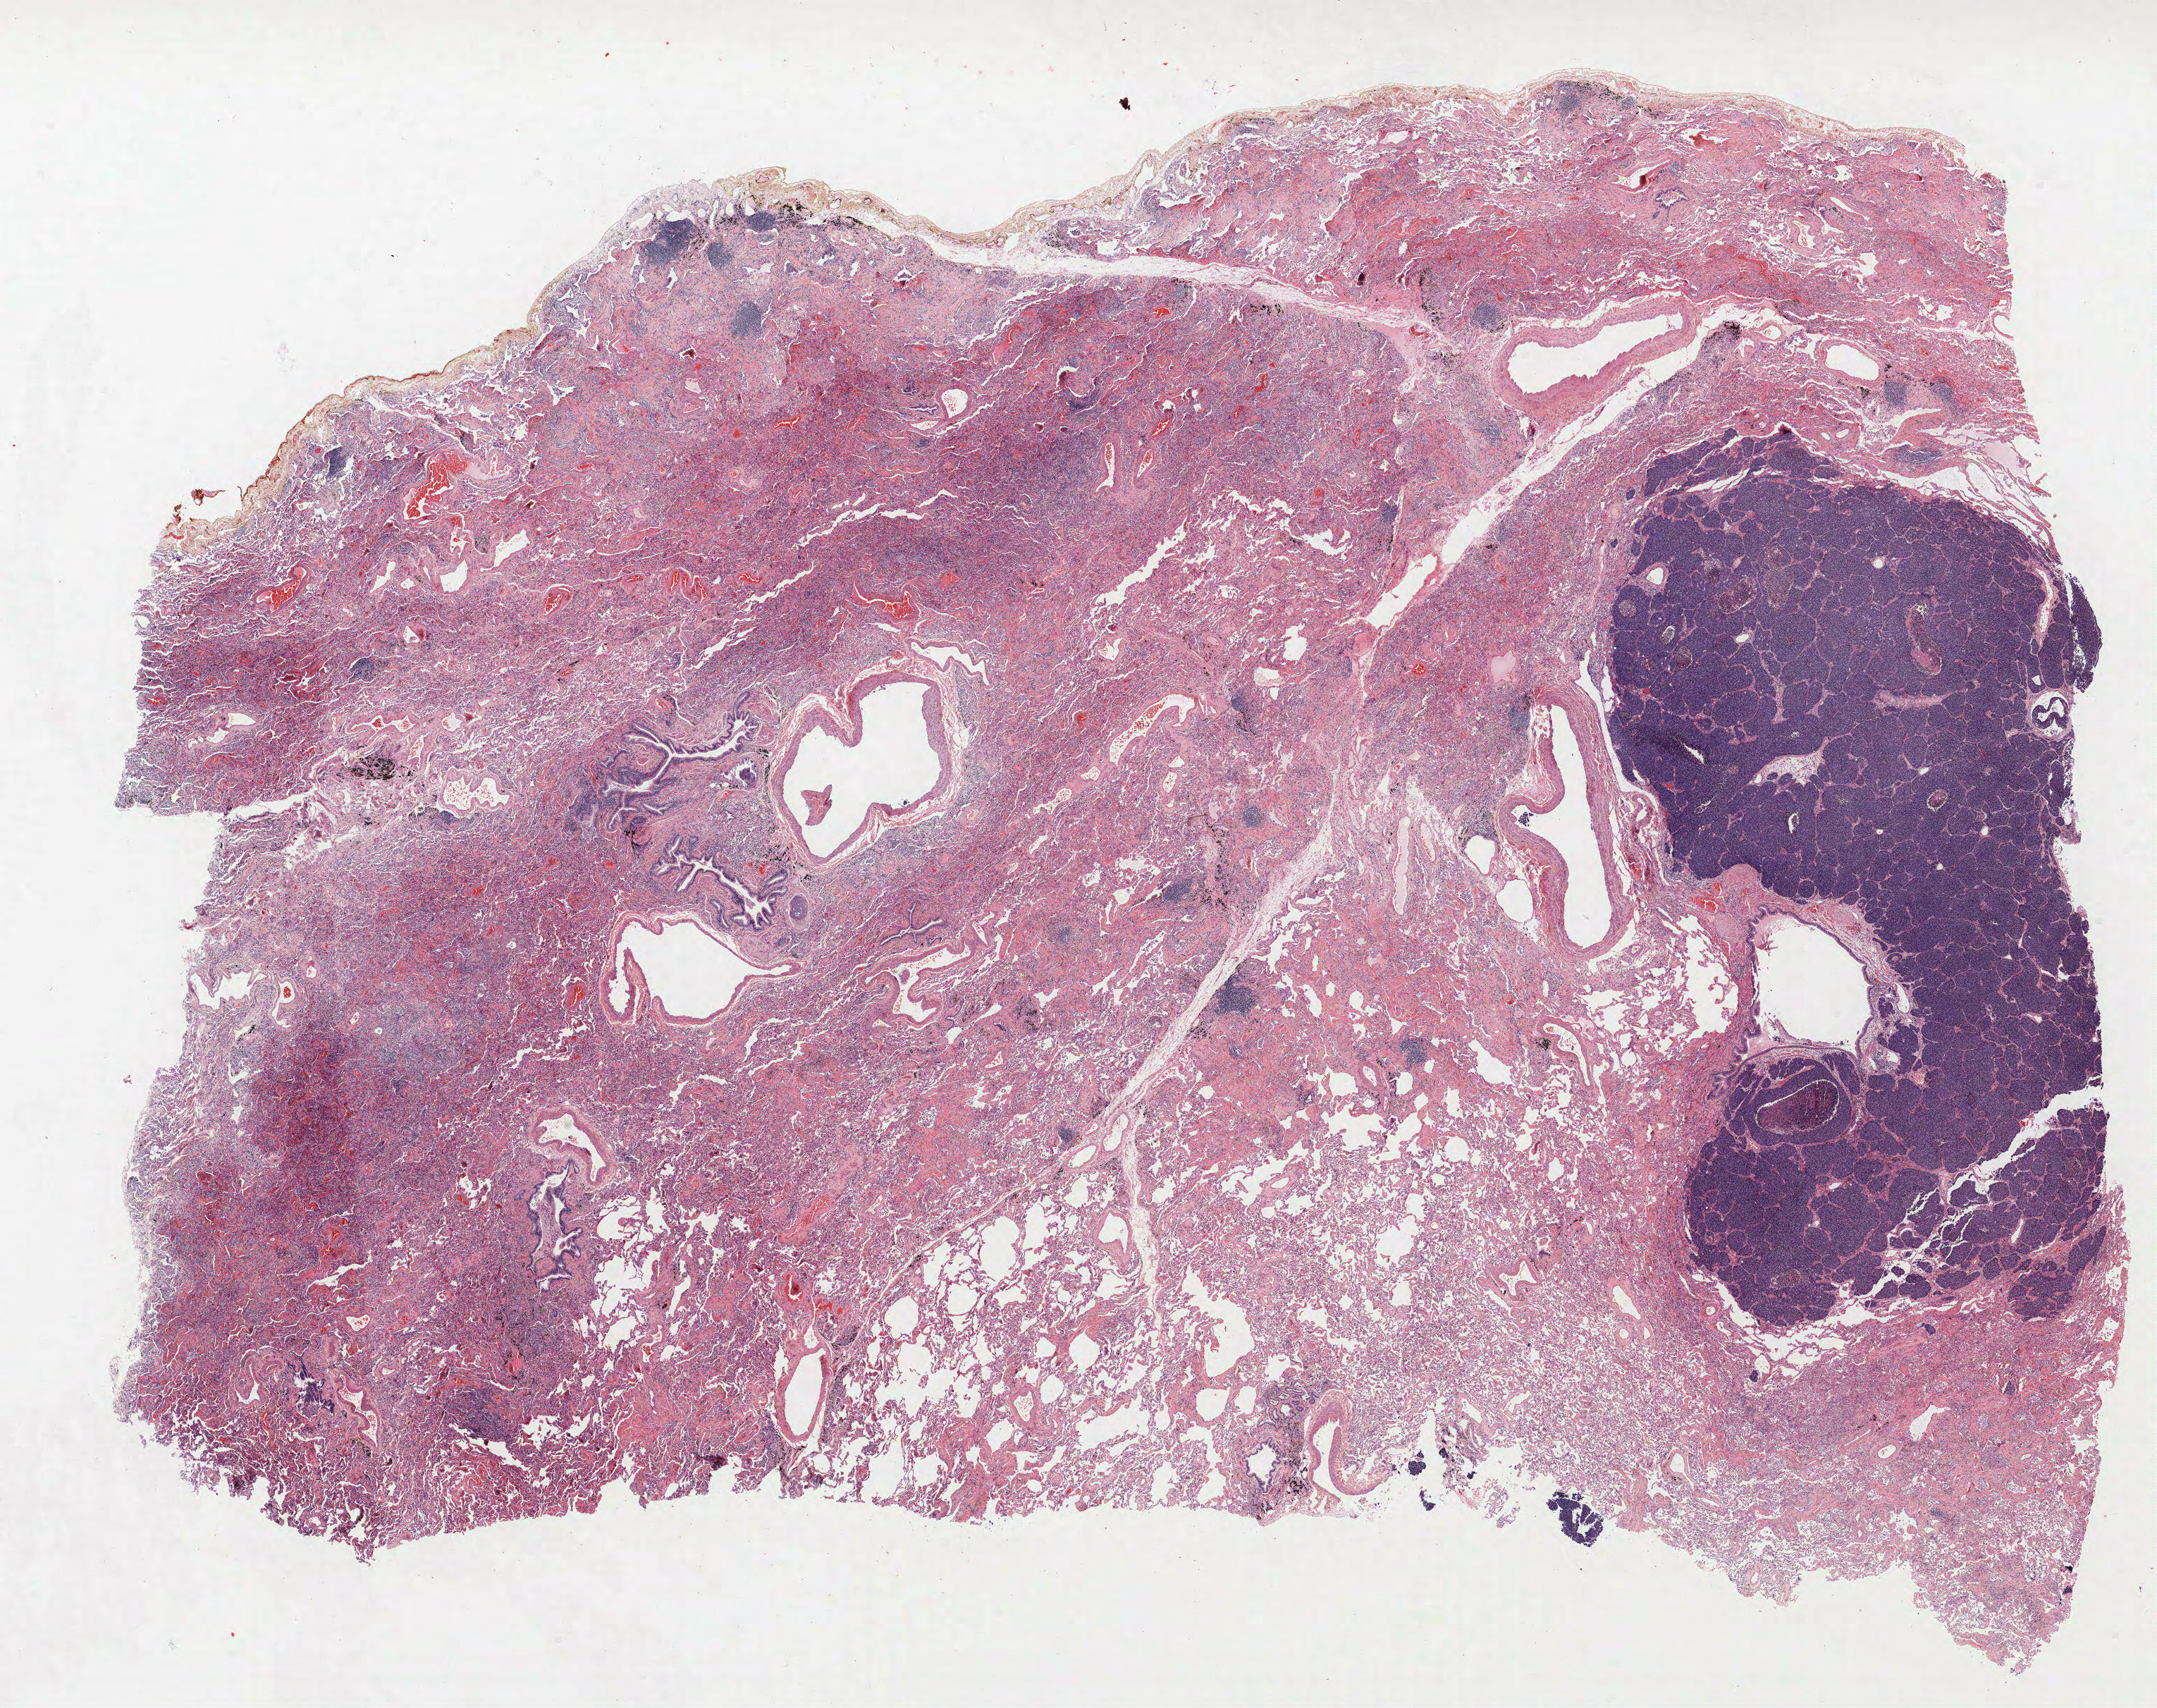
Whole-slide histology image, H&E — shown as a low-resolution overview of the whole scanned area (about 24.5 x 19.4 mm, acquisition: 40x scan); FFPE section; lung tissue. Male, age 68 at enrolment. Current smoker at enrolment. Grade: undifferentiated (G4).
Primary tumour location (clinical record): lingula. Participant's lung-cancer diagnosis: Large cell neuroendocrine carcinoma. Stage (AJCC 6th edition): IA. Tumour size (pathology): 25 mm.